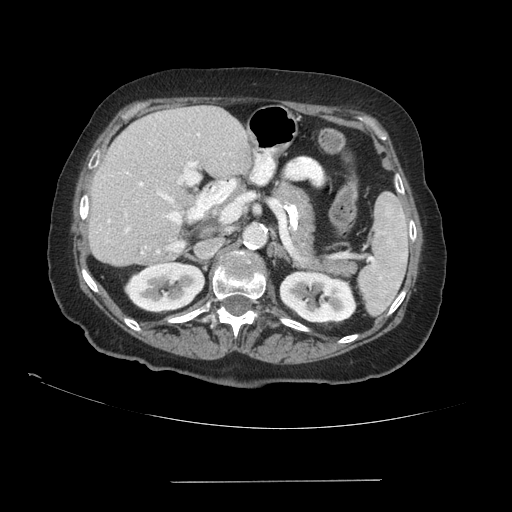
Contrast-enhanced abdominal CT (liver protocol), one axial slice. Position 52 of 89 along the scan axis. Reconstruction kernel STANDARD. Soft-tissue window (W 400 / L 40 HU). 2.5 mm slice thickness. 512 × 512 image matrix. Case-level facts recorded for this patient, not image findings: diagnosis: hepatocellular carcinoma (patient treated with transarterial chemoembolisation; whether this scan precedes or follows treatment is not stated here); TNM stage (as recorded): Stage-IVA; Child-Pugh class: A; tumour differentiation: poorly differentiated; tumour nodularity: uninodular.
Structures marked on this image (semi-automatic segmentation, software-assisted and operator-edited):
- liver parenchyma outside the tumour (the mass and vessels are separate outlines, so this box may not span the whole liver): box from (x=88, y=106) to (x=250, y=266) px
- liver vessels: (x=108, y=133)–(x=200, y=253)